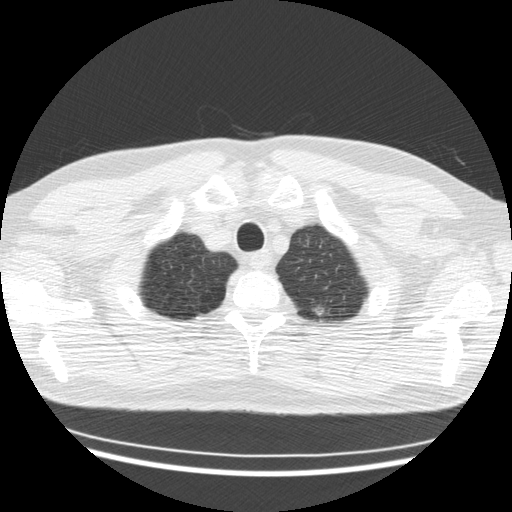
Low-dose screening chest CT, axial slice, second screening round (one year after baseline), lung window (W 1500 / L -600 HU), 2.5 mm slice thickness, 120 kVp, slice 21 of 176 in the series. Male participant, aged 57 years at enrolment. Former smoker at enrolment.
- Expert-annotated lung lesion, box from (x=304, y=298) to (x=336, y=325) px.
- The screening reader recorded 2 non-calcified nodules or masses ≥4 mm on this exam (right upper lobe, right lower lobe); which of them this box marks is not recorded.
- Lung cancer was diagnosed 332 days after this screen: adenocarcinoma, NOS, left upper lobe, stage IV (AJCC 6th edition), 50 mm at pathology.